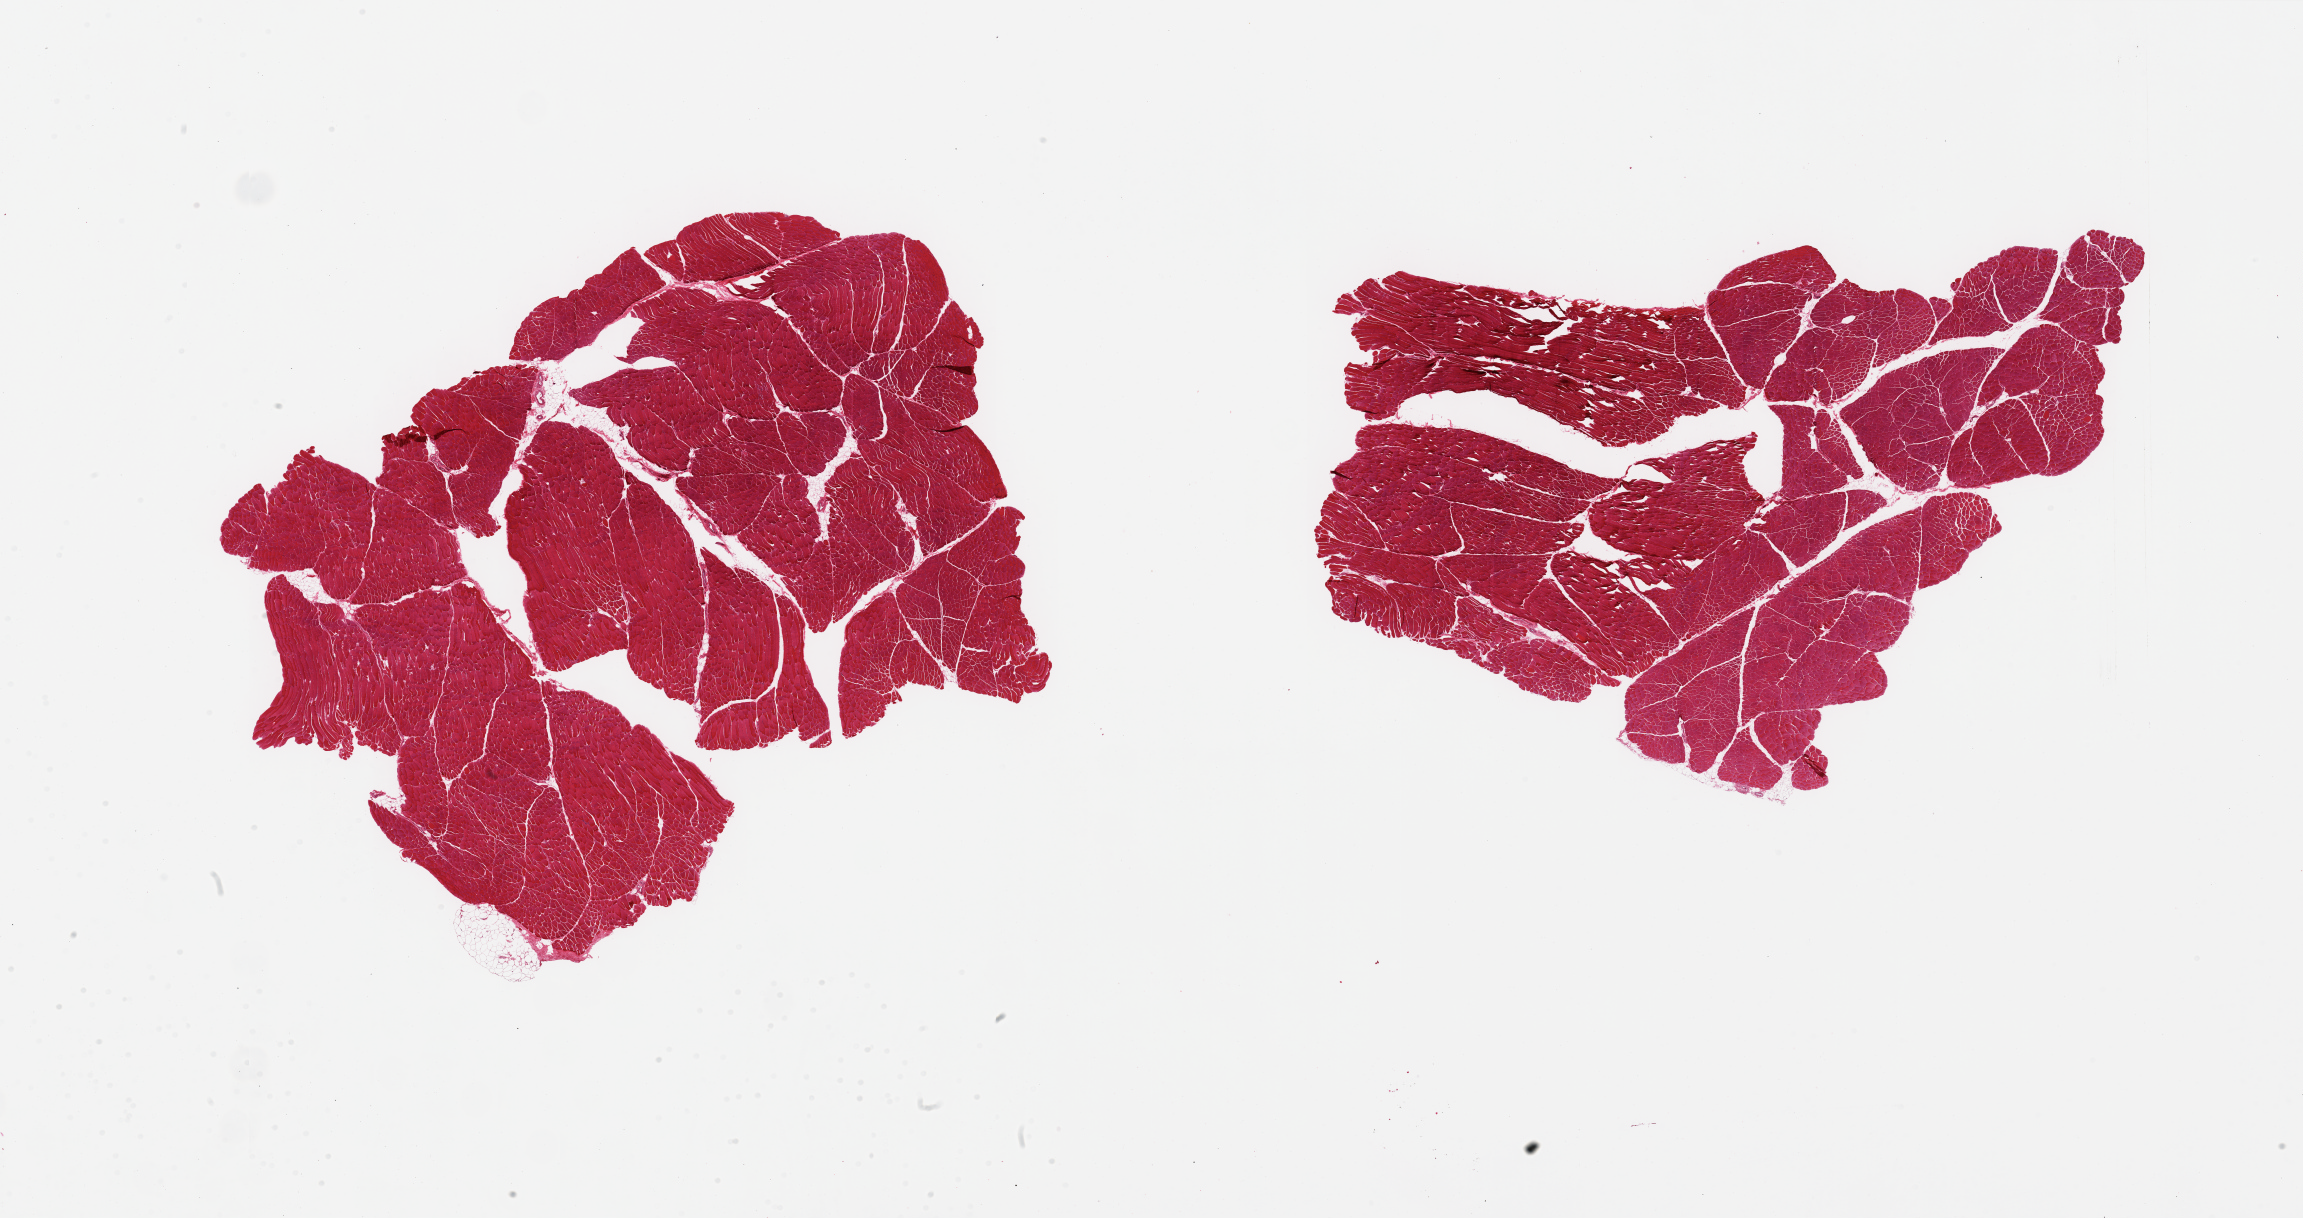
Whole-slide image, hematoxylin and eosin (H&E) stain — a low-resolution overview of the entire scanned area, about 36.4 x 19.3 mm (from a 20x scan); PAXgene-fixed, paraffin-embedded tissue; target tissue: skeletal muscle; tissue donor sample.
Pathologist's review note for this sample: 2 pieces, trace interstitial fat.